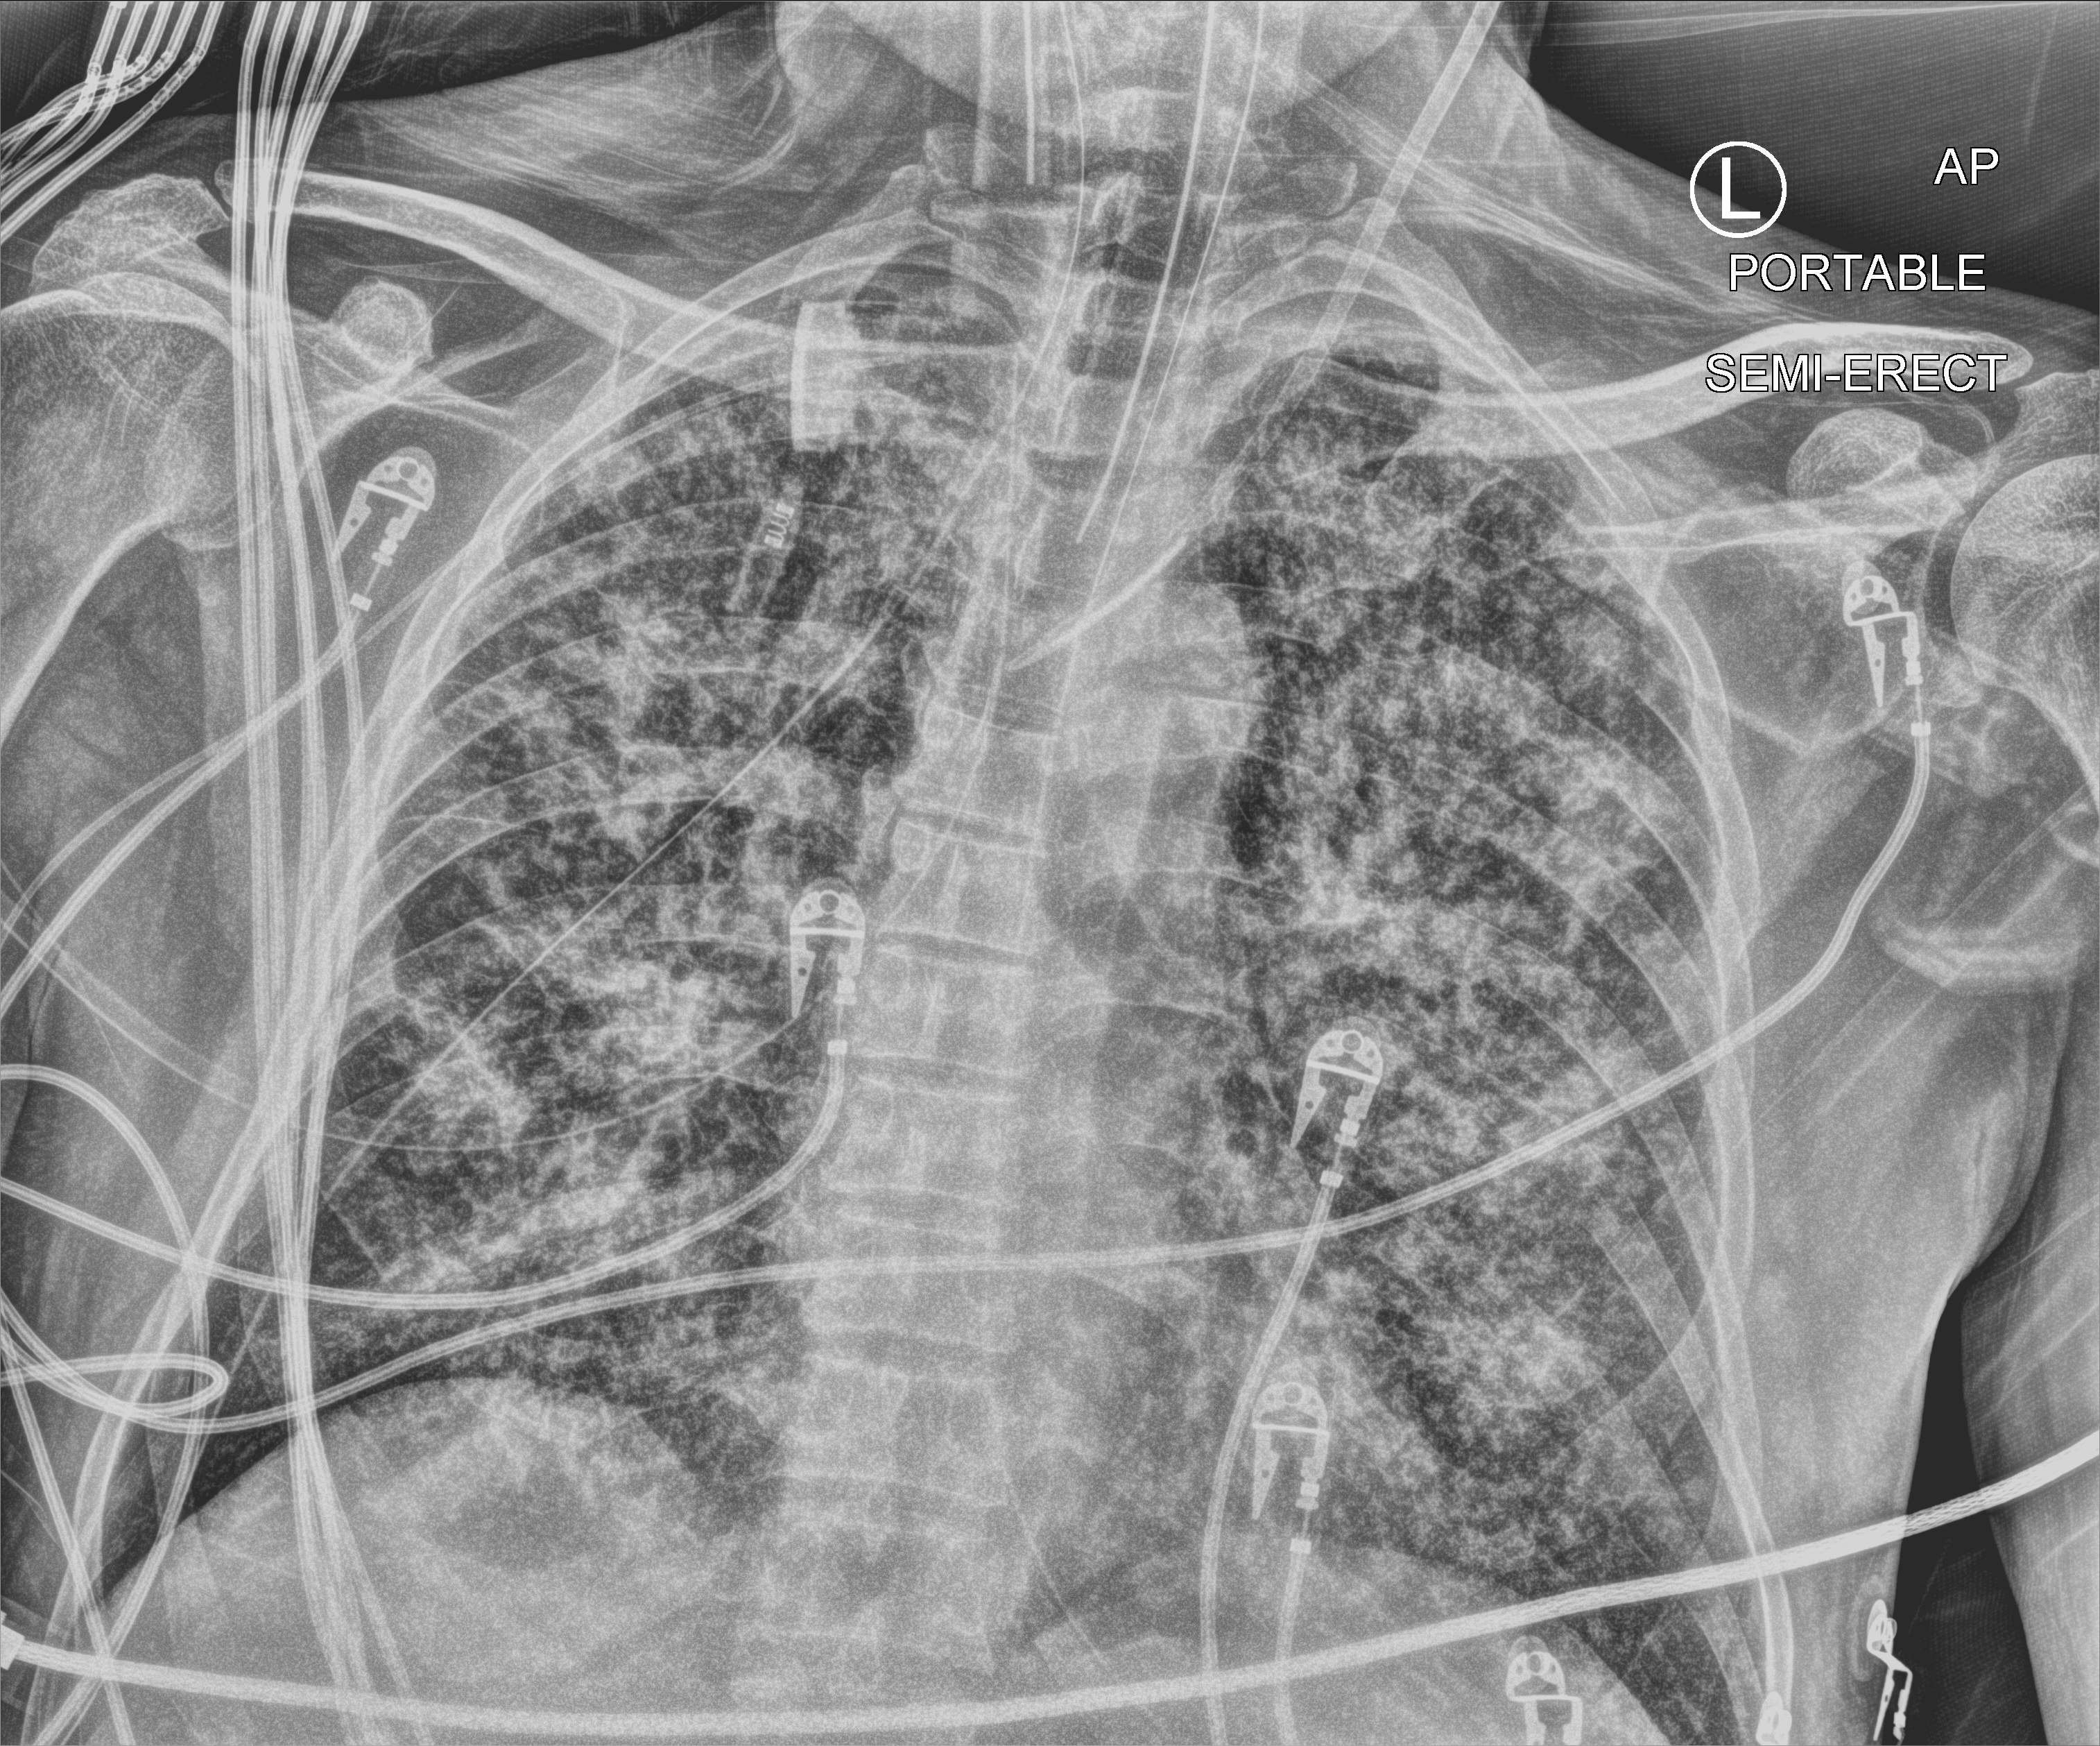
Portable chest radiograph, anteroposterior (AP) projection. Male patient hospitalised with COVID-19, age 60–74 years.
Hospital-stay facts (about this admission, not read from this image; timing relative to this image not recorded):
- admitted to intensive care during this hospital stay: yes